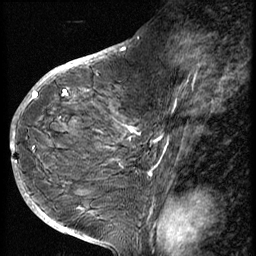
Breast MRI (dynamic contrast-enhanced), one sagittal slice; 3 images stored at this slice position (order not interpretable as contrast timing); 1.5 T; TE 4.2 ms, TR 9 ms; 2.5 mm slice thickness; 256 × 256 image matrix, field of view 180 × 180 mm. Female patient, age 49 years. From the clinical record (not read from this slice): setting: breast cancer imaged before/during neoadjuvant chemotherapy; receptor status: HER2-positive.
Outlined on this slice (semi-automatically segmented with operator editing):
- analysis volume of interest (the breast-tissue region the enhancement analysis was run in; not a lesion): box from (x=37, y=85) to (x=132, y=207) px
- tumour enhancement mask (voxels above the 140 % enhancement threshold inside the analysis volume of interest): (x=37, y=90)–(x=131, y=132)